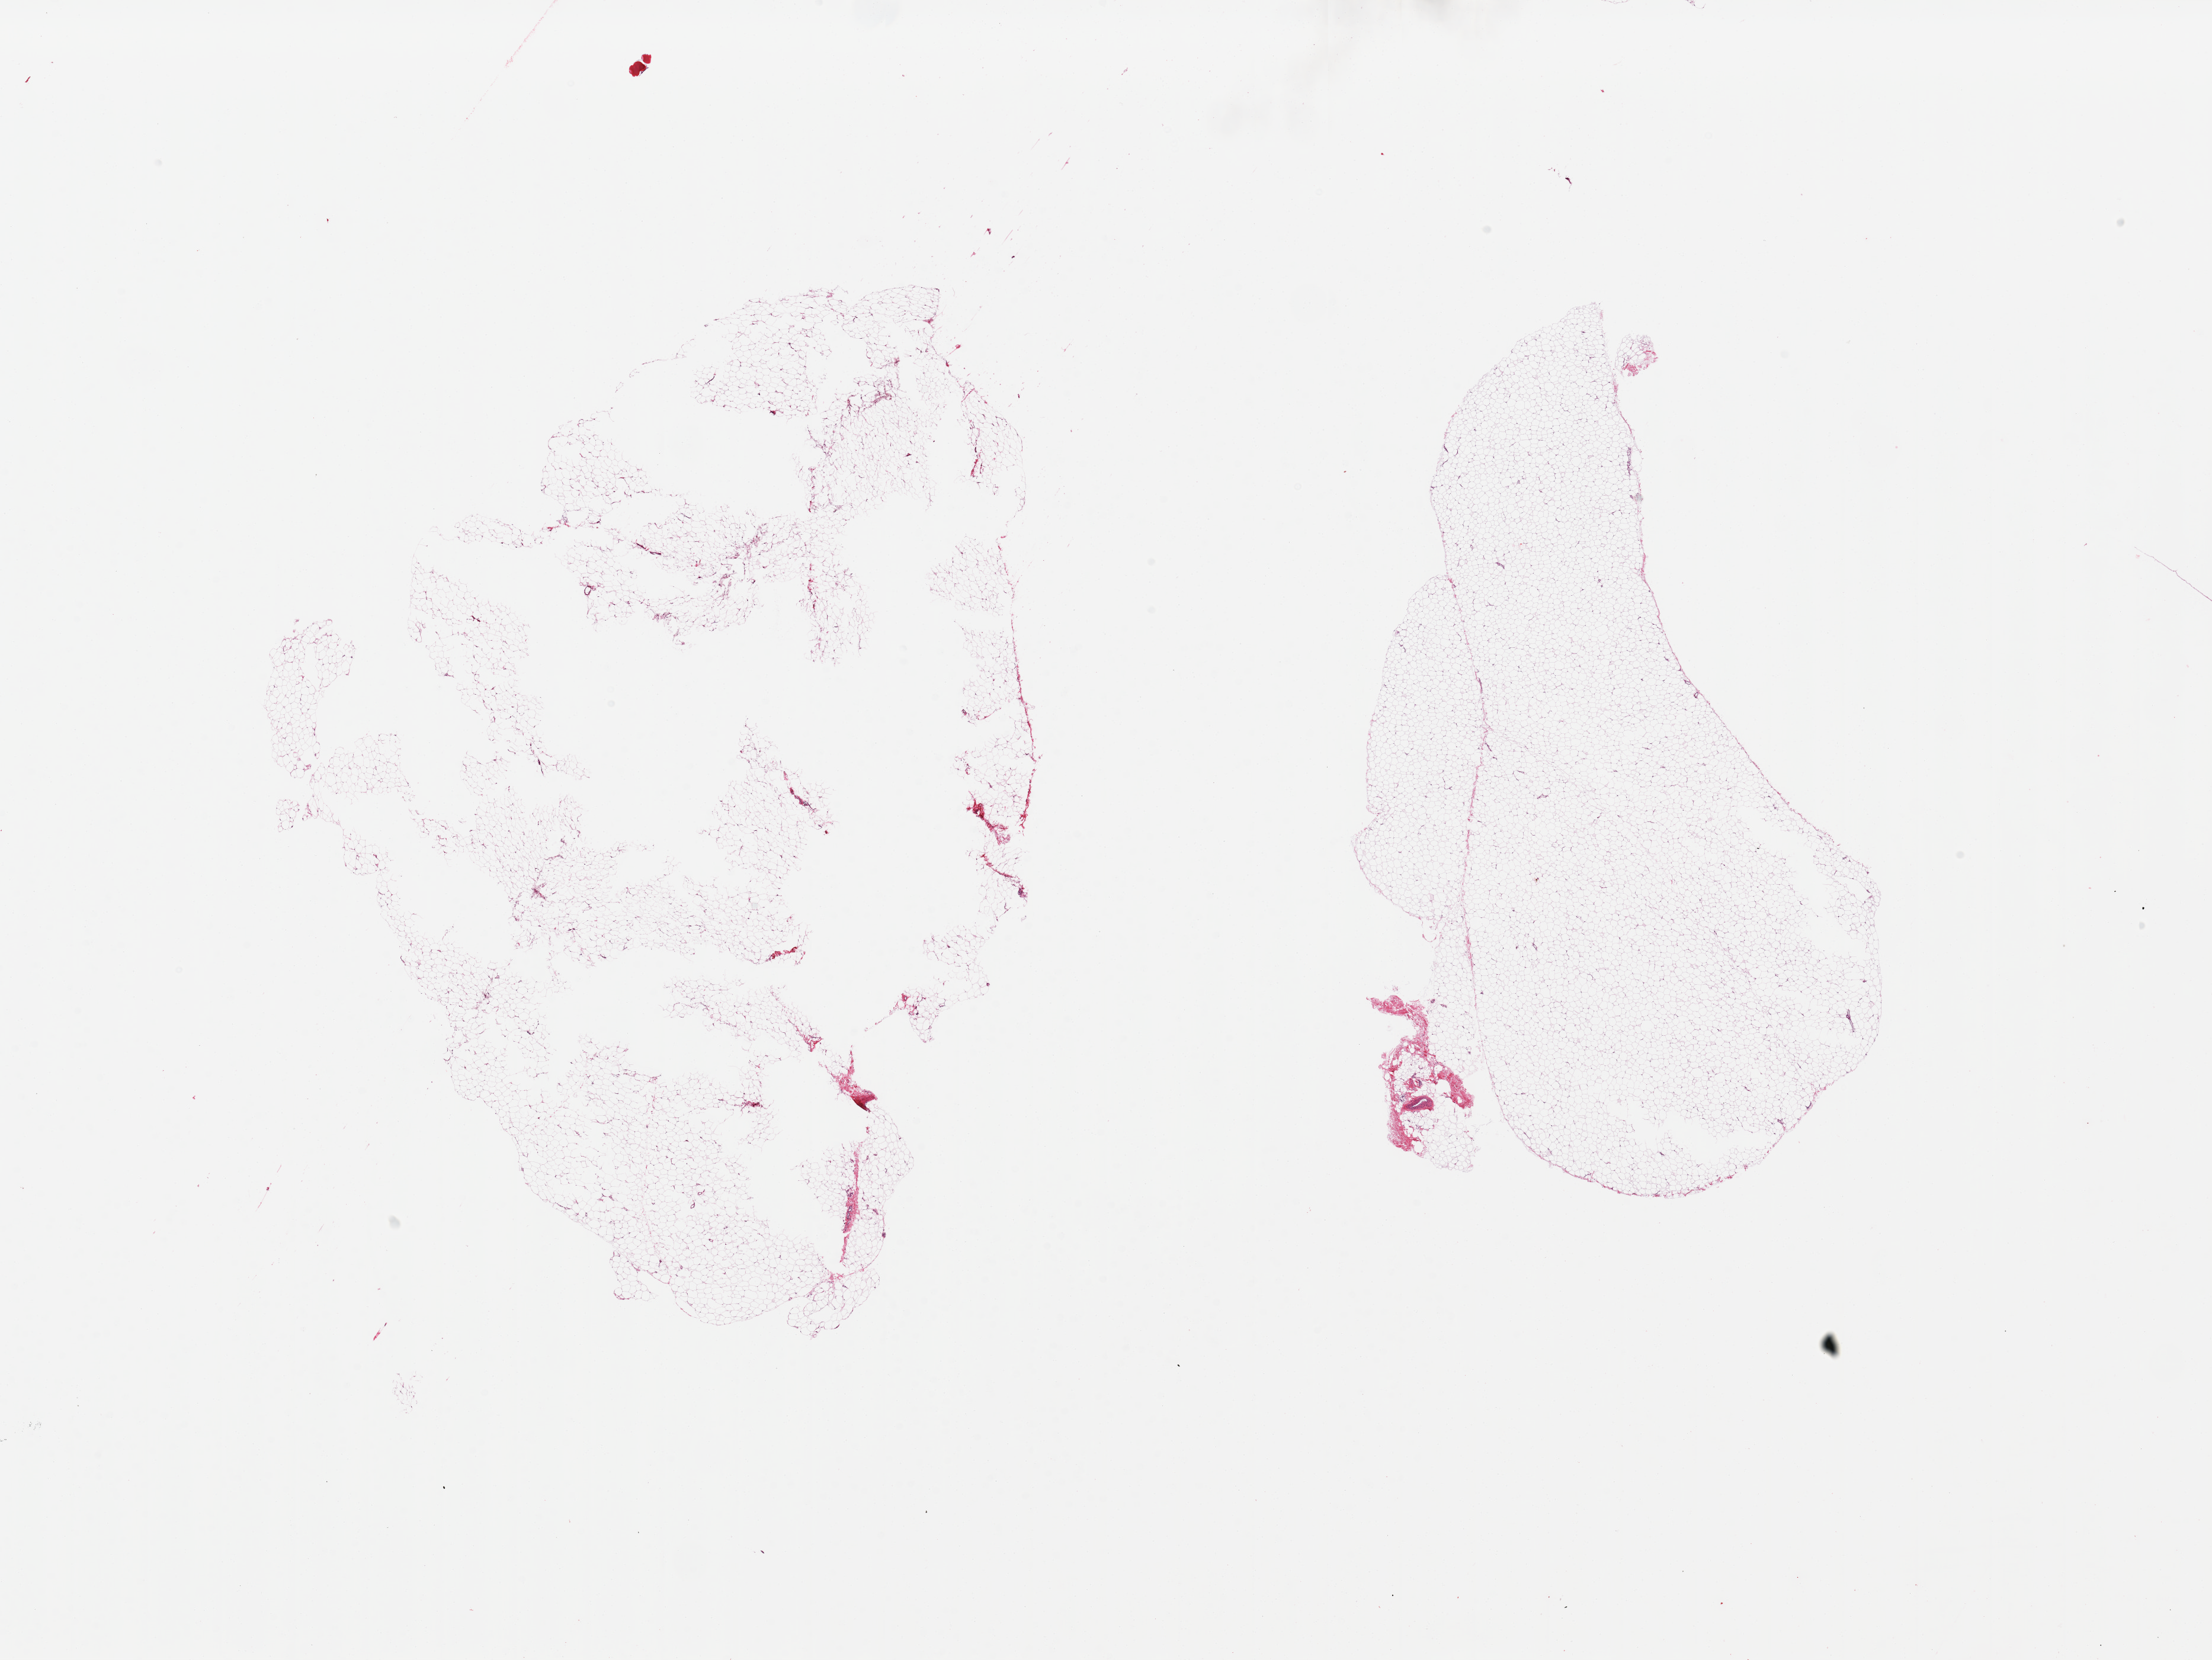
Digitized haematoxylin and eosin-stained section, brightfield — low-resolution overview of the scanned area, about 29.5 x 22.2 mm (from a 20x scan); PAXgene-fixed, paraffin-embedded tissue; target tissue: adipose tissue; tissue donor sample. Donor: female.
Pathologist's review note for this sample: 2 pieces; central defects, mature fat.